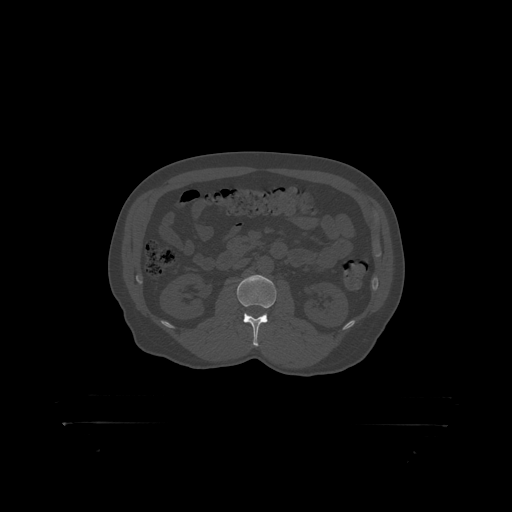
CT including the spine, one axial slice; slice 291 of 399 in the series (ordered by position); 120 kVp; bone window (W 1800 / L 400 HU); 512 × 512 image matrix, field of view 650 × 650 mm. Male patient, age 46 years. Case-level facts recorded for this patient, not image findings: primary cancer: skin.
Annotated regions visible in this slice (semi-automatically segmented with operator editing):
- L2 vertebra: bounding box [x1, y1, x2, y2] px = [237, 276, 277, 319]